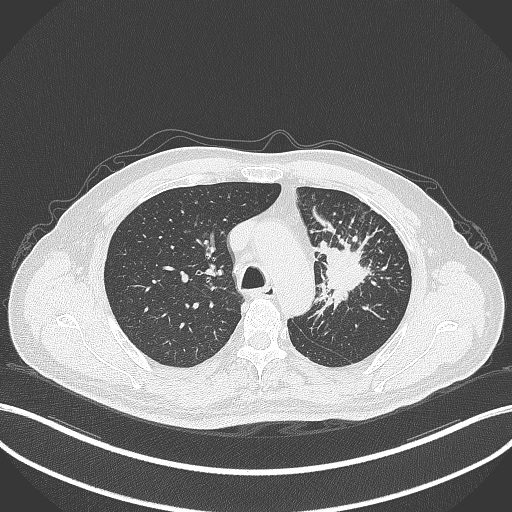
Chest CT, one axial slice. Slice 257 of 386 in the series (ordered by position). Lung window (W 1500 / L -600 HU). 512 × 512 image matrix, field of view 400 × 400 mm. Patient: male, 69 years. From the clinical record (not read from this slice): clinical TNM (as recorded): T2a N2 M0.
Structures marked on this image (rectangle marked by the reading radiologist):
- lung tumour (recorded histology: adenocarcinoma): bounding box (x1, y1, x2, y2) in pixels: (319, 238, 375, 308)